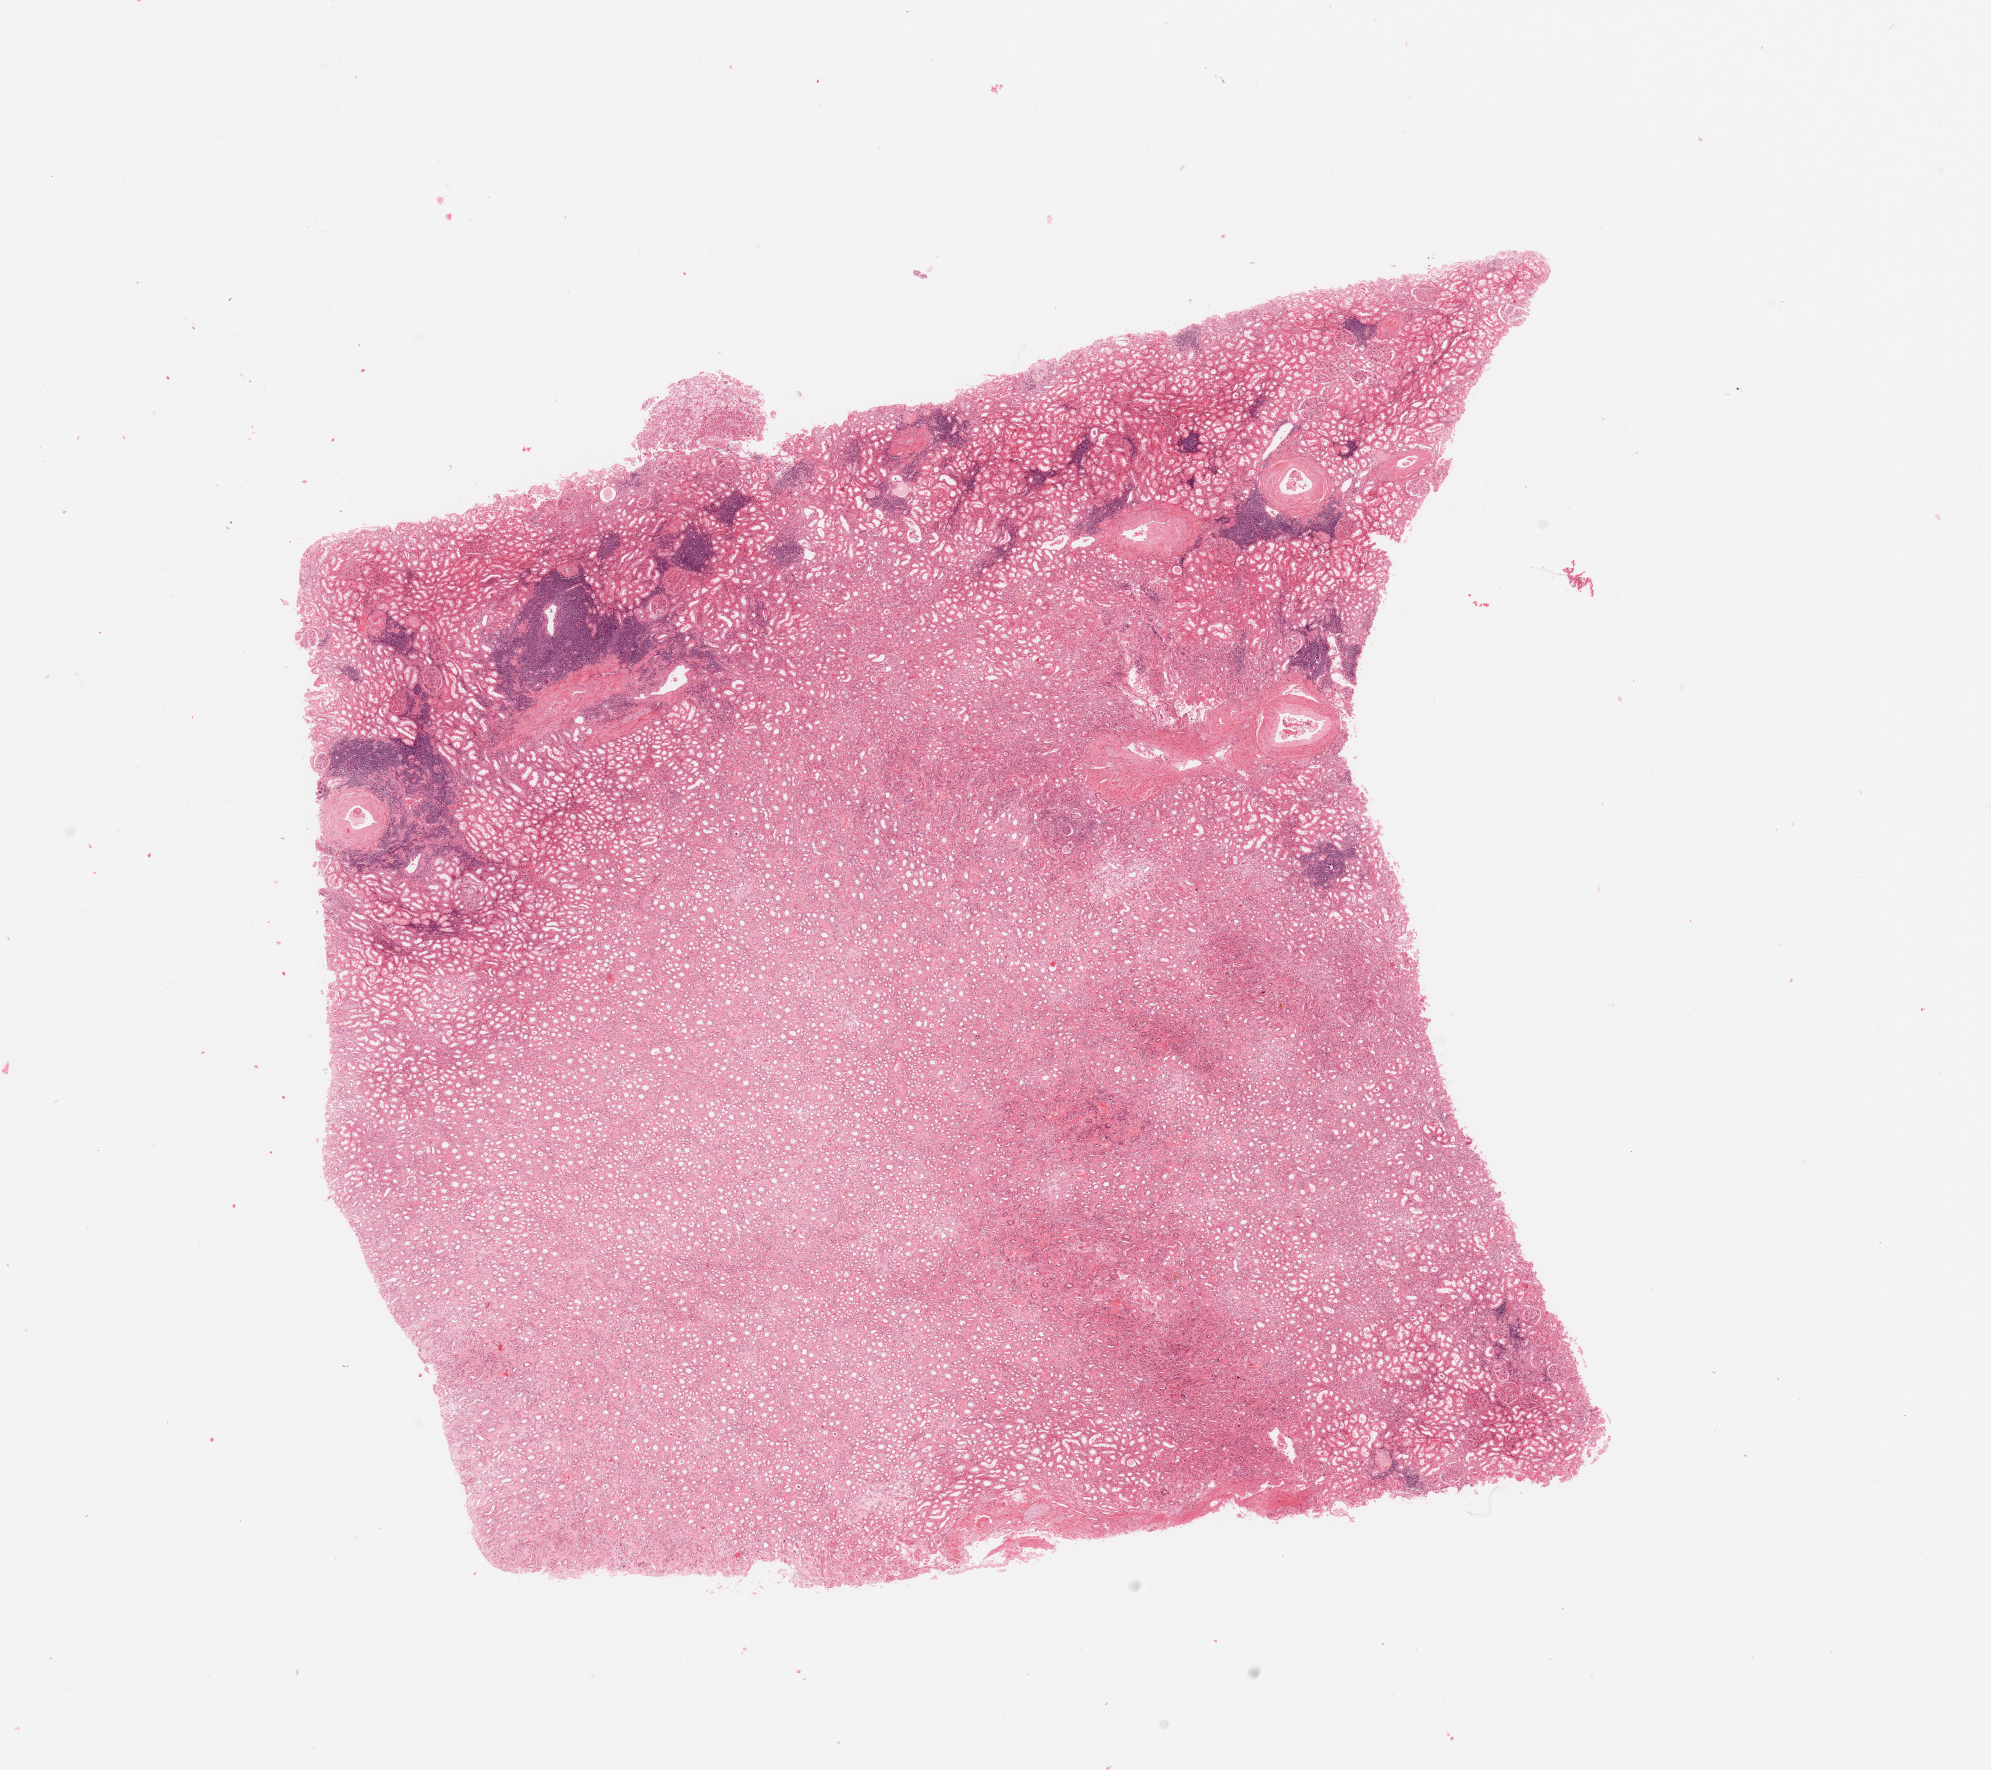
Hematoxylin and eosin (H&E) stained whole-slide image — whole scanned area (about 15.8 x 14.0 mm) shown as a low-resolution overview. Normal (non-tumour) tissue sample, kidney. 68-year-old male patient.
This section: normal (non-tumour) tissue from the same patient. Patient diagnosis: Renal cell carcinoma, NOS.